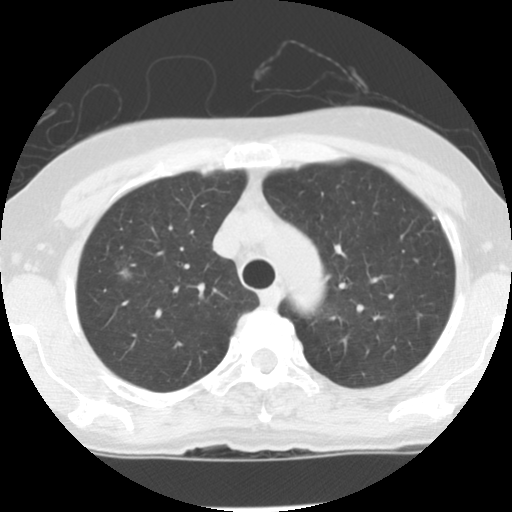
Chest CT (low-dose screening protocol), one axial image, baseline annual screen, lung window (W 1500 / L -600 HU), standard (soft-tissue) reconstruction kernel (STANDARD), 120 kVp, 512 × 512 image matrix. Female participant, aged 62 years at enrolment.
Expert-annotated lung lesion, bounding box [x1, y1, x2, y2] px = [104, 252, 144, 293]. The exam's reader record, not a measurement of the box and not confirmed to be the same lesion: non-calcified nodule or mass ≥4 mm, right upper lobe, 7 × 5 mm, poorly defined margins, ground glass attenuation. Official screen result: positive, change unspecified: nodule(s) >= 4 mm or enlarging nodule(s), mass(es), or other non-specific abnormalities suspicious for lung cancer. Later outcome: lung cancer diagnosed 875 days after this screen — bronchiolo-alveolar adenocarcinoma, NOS, right upper lobe, stage IA (AJCC 6th edition), 10 mm at pathology.